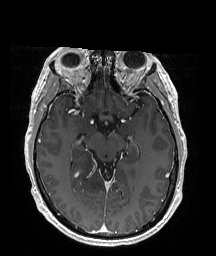
Brain MRI from a brain-tumour surgery series, one axial slice. Position 109 of 176 along the scan axis. T1-weighted post-contrast. 1 mm slice thickness. 216 × 256 image matrix, field of view 211 × 250 mm. Case-level facts recorded for this patient, not image findings: histopathology: Oligodendroglioma; WHO grade: 2; IDH mutation: yes; tumour location: Right Parietal.
Structures marked on this image (outlined manually by an expert reader):
- tumour: bounding box (x1, y1, x2, y2) in pixels: (70, 150, 111, 205)